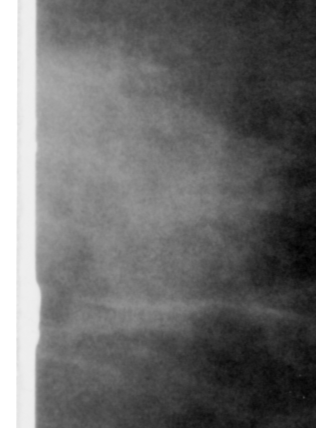
Region of interest cut from a scanned film mammogram (one marked finding), left breast, MLO view, BI-RADS breast density category 3 (scale 1–4).
Finding: mass, shape irregular, margins ill defined; BI-RADS assessment category 0 (incomplete: needs additional imaging); subtlety rating 4 on a 1 (subtle) to 5 (obvious) scale; pathology result (as recorded, not read from the image): benign.